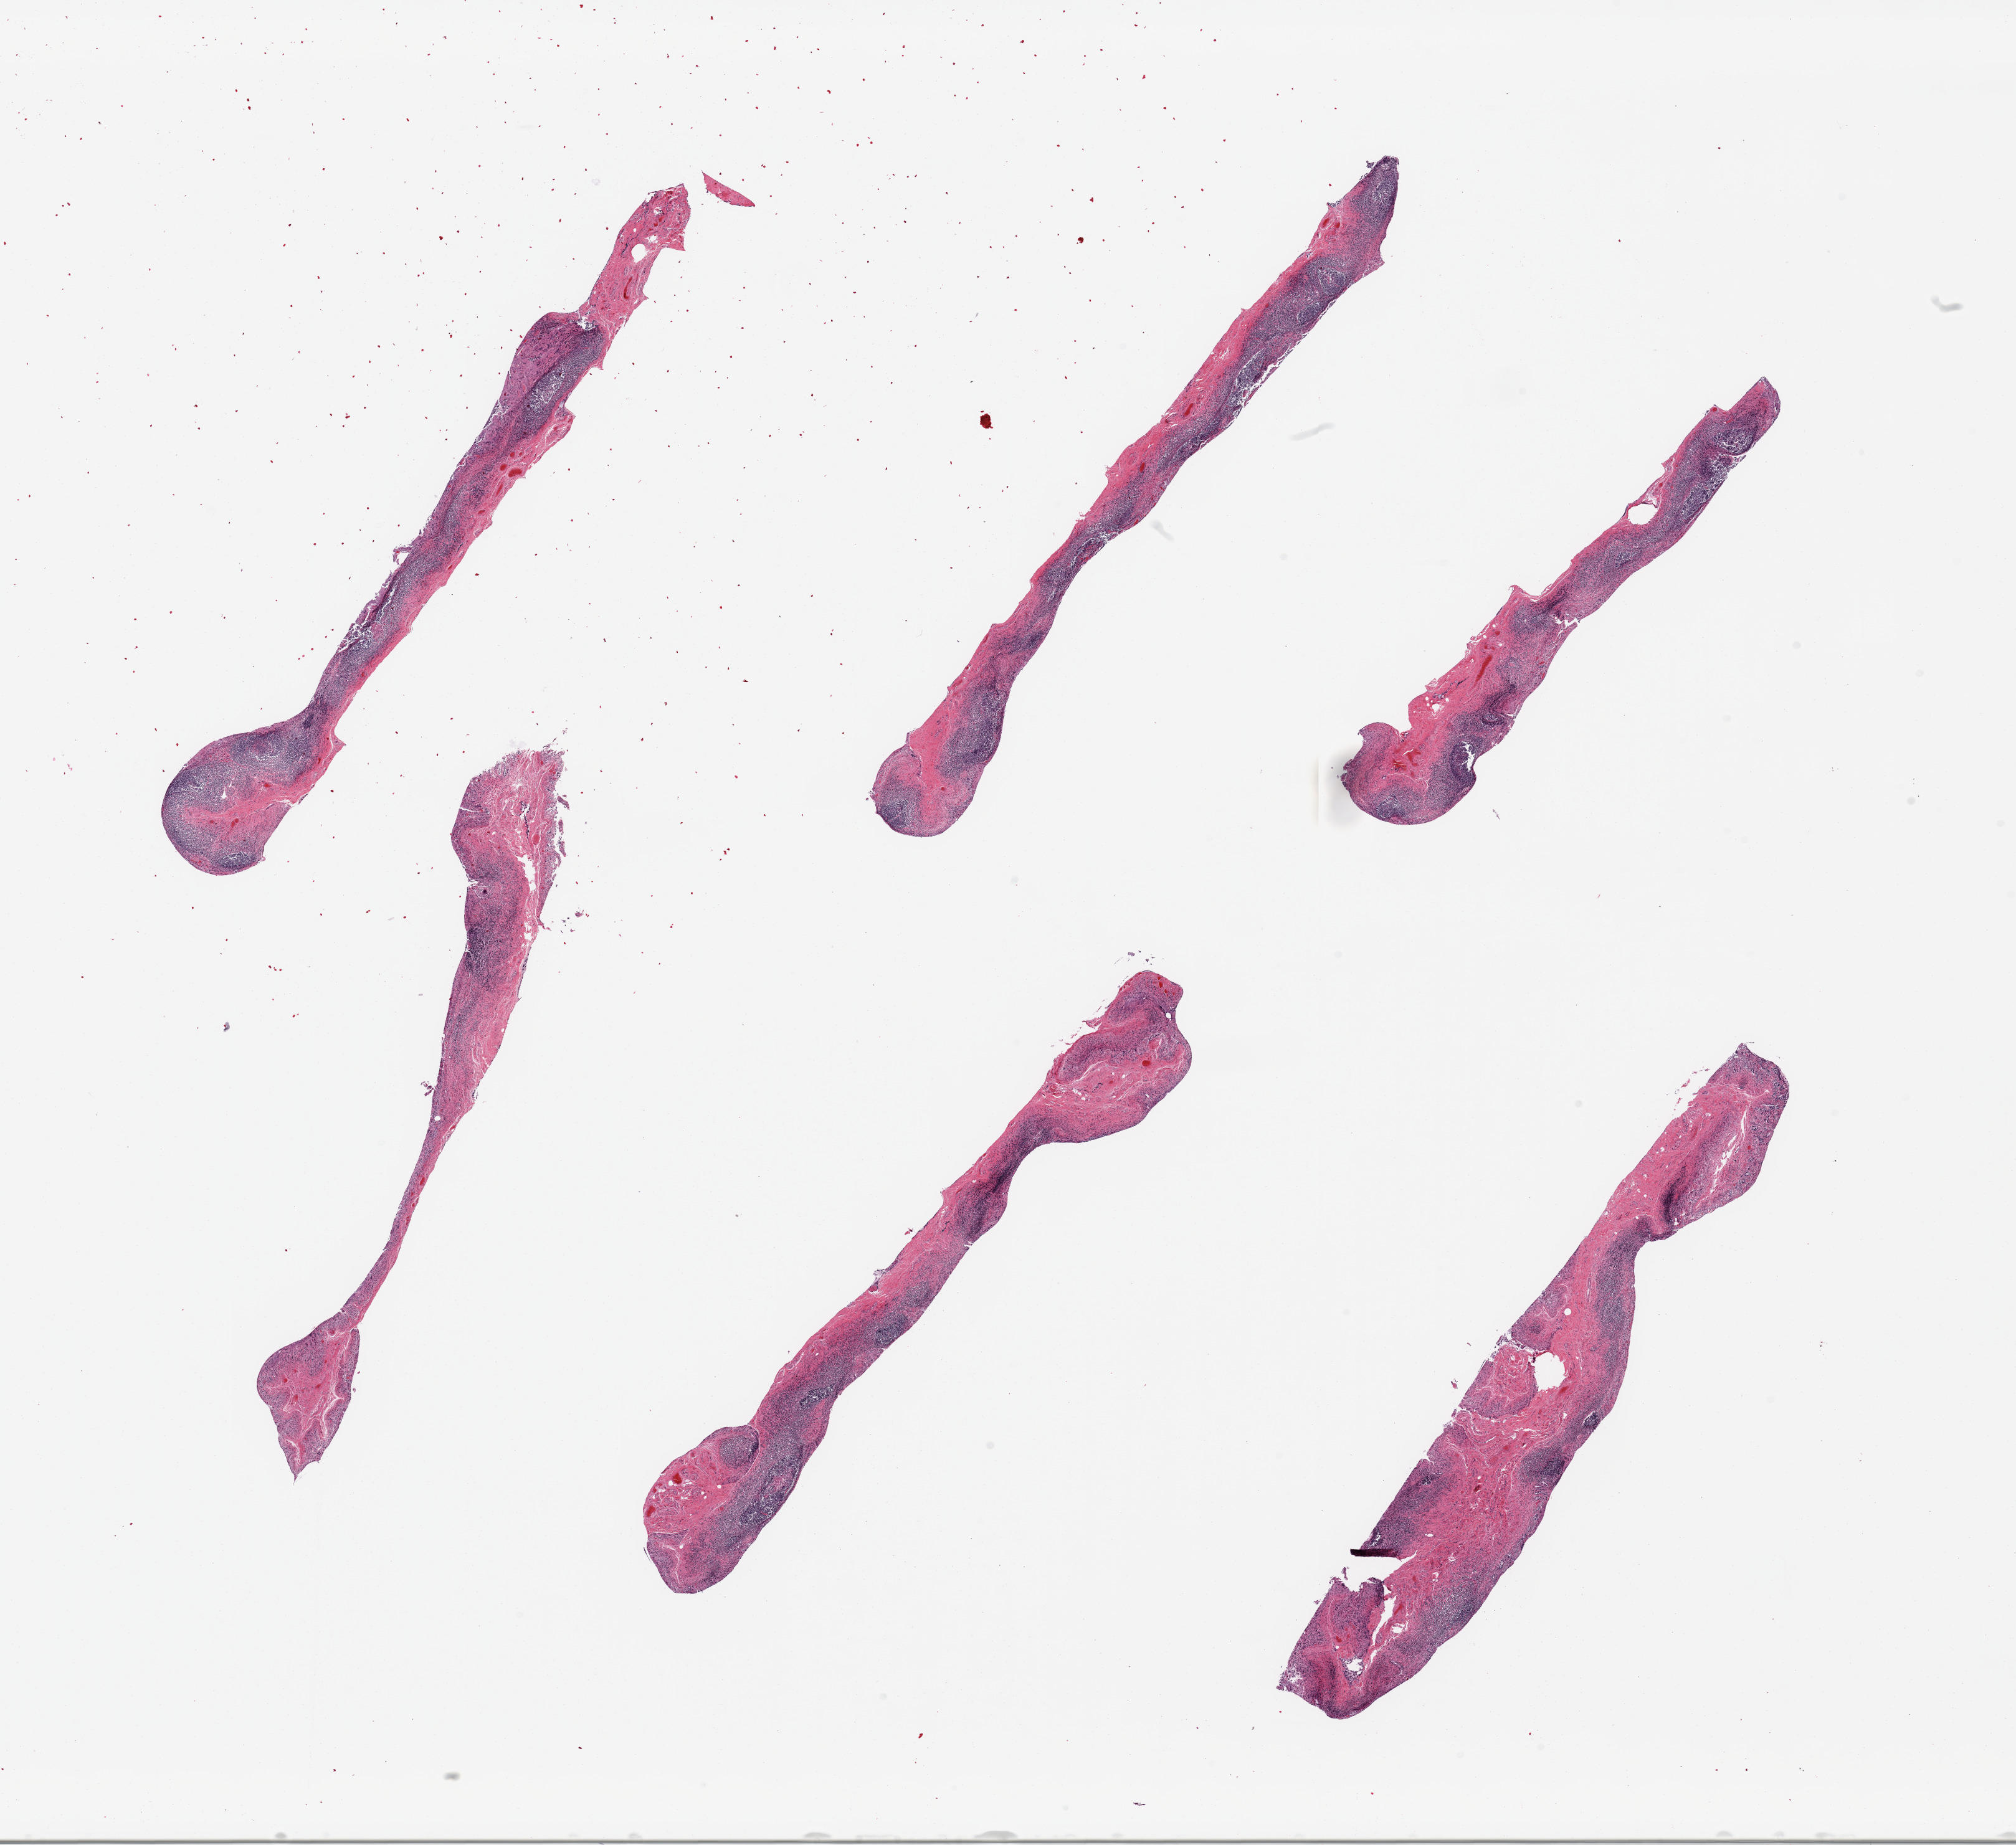
Whole-slide image, haematoxylin and eosin stain — shown as a low-resolution overview of the whole scanned area (about 25.6 x 23.4 mm, from a 20x scan); PAXgene-fixed paraffin-embedded (PFPE) section; sampled site (target tissue): ileum; tissue donor sample. Donor: male.
Pathologist's review note for this sample: 6 pieces; well dissected with abundant lymphoid tissue.